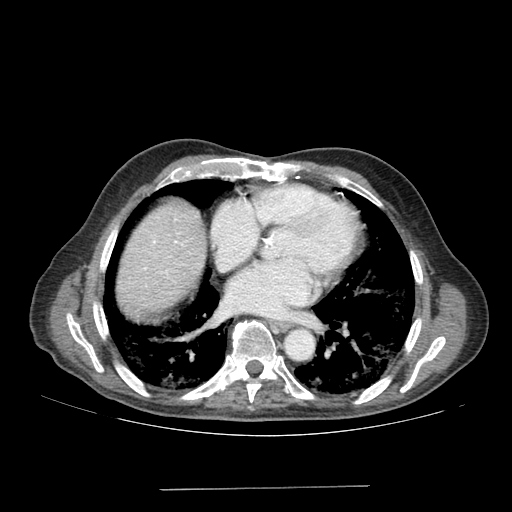
Contrast-enhanced abdominal CT (liver protocol), one axial slice; slice 174 of 192 in the series (ordered by position); soft-tissue window (W 400 / L 40 HU); 2.5 mm slice thickness; 512 × 512 image matrix, field of view 400 × 400 mm. Case-level facts recorded for this patient, not image findings: diagnosis: hepatocellular carcinoma (patient treated with transarterial chemoembolisation; whether this scan precedes or follows treatment is not stated here); TNM stage (as recorded): Stage-IVA; Child-Pugh class: A; tumour differentiation: poorly differentiated; tumour nodularity: uninodular.
Annotated regions visible in this slice (semi-automatically segmented with operator editing):
- liver parenchyma outside the tumour (the mass and vessels are separate outlines, so this box may not span the whole liver): bounding box [x1, y1, x2, y2] px = [116, 202, 206, 312]
- liver vessels: [145, 241, 177, 269]